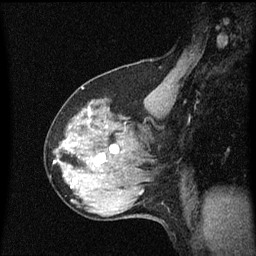
Breast MRI (dynamic contrast-enhanced), one sagittal slice. Slice 36 of 60 in the series (ordered by position). Dynamic contrast-enhanced series, image 2 of 3 at this slice position (ordered by acquisition). 1.5 T. TE 4.2 ms, TR 8.4 ms. 256 × 256 image matrix, field of view 200 × 200 mm. Patient: female, 64 years. Case-level facts recorded for this patient, not image findings: setting: breast cancer imaged before/during neoadjuvant chemotherapy; receptor status: HR-positive, HER2-negative.
Annotated regions visible in this slice (semi-automatic segmentation, software-assisted and operator-edited):
- analysis volume of interest (the breast-tissue region the enhancement analysis was run in; not a lesion): bounding box (x1, y1, x2, y2) in pixels: (56, 100, 142, 175)
- tumour enhancement mask (voxels above the 70 % enhancement threshold inside the analysis volume of interest): (97, 160, 100, 167)